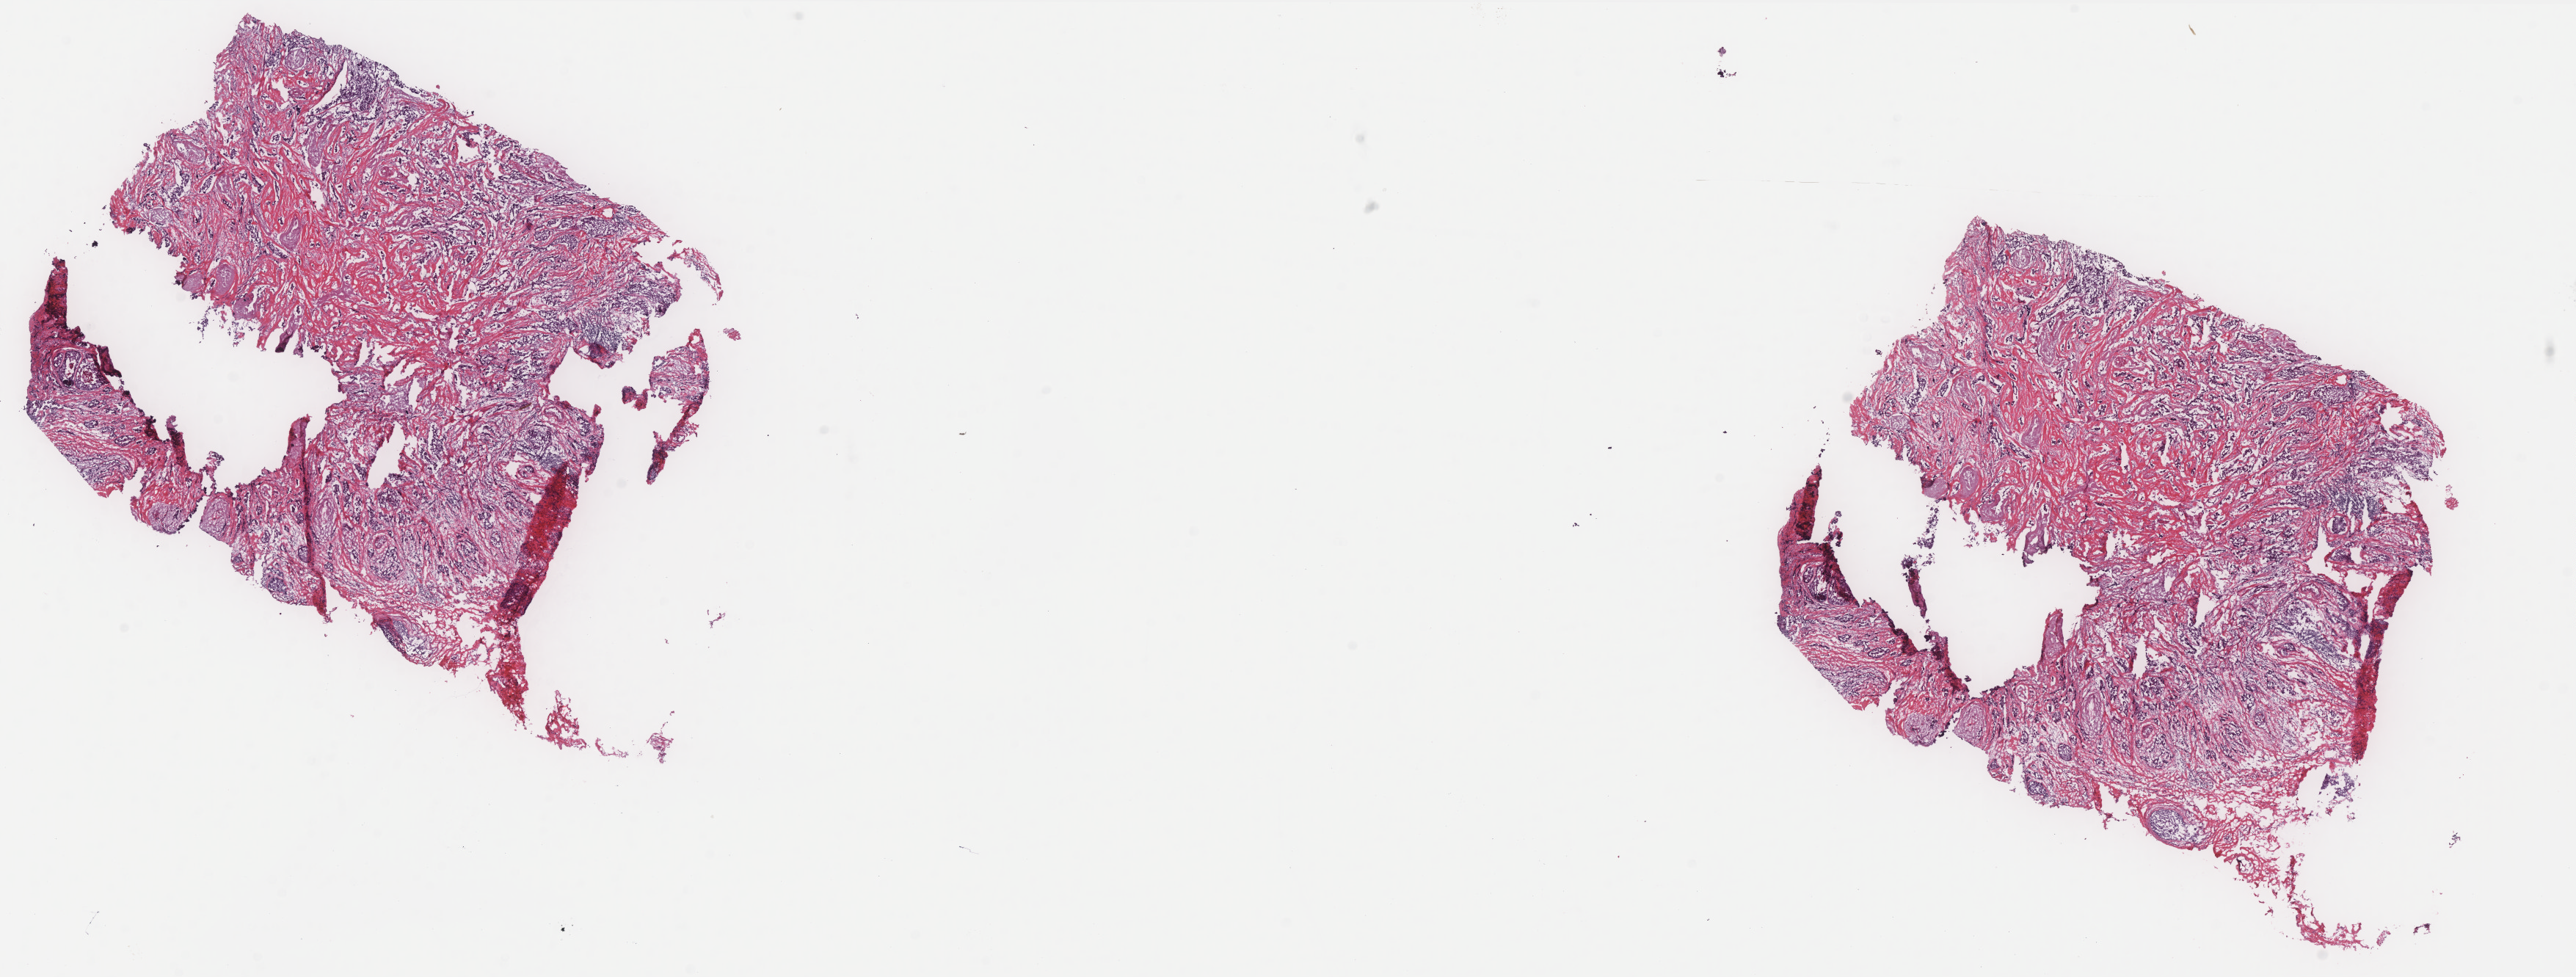
Whole-slide histology image, H&E — a low-resolution overview of the entire scanned area, about 28.1 x 10.7 mm (acquisition: 40x scan). Frozen section from the bottom of the tissue portion. Primary tumour sample from the breast. Female, age 67 years at initial diagnosis. Composition of this section per pathologist review: tumour cells 80%, tumour nuclei 80%, normal cells 0%, stromal cells 20%, necrosis 0%. Infiltration values recorded for this section: lymphocyte infiltration 2%, monocyte infiltration 1%, neutrophil infiltration 1%.
AJCC pathologic stage: IIIA. Pathologic diagnosis: Infiltrating duct carcinoma, NOS. Lymph nodes positive (case pathology): 7 of 16 examined.